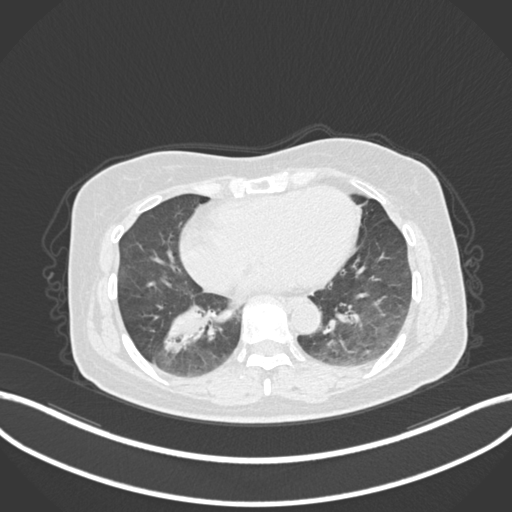
Chest CT, one axial slice. Slice 50 of 222 in the series (ordered by position). 120 kVp. Lung window (W 1500 / L -600 HU). 512 × 512 image matrix, field of view 400 × 400 mm. Patient: female, 67 years. From the clinical record (not read from this slice): clinical TNM (as recorded): T1c N1 M0.
Structures marked on this image (bounding box drawn by a radiologist):
- lung tumour (recorded histology: adenocarcinoma): bounding box [x1, y1, x2, y2] px = [159, 300, 215, 356]